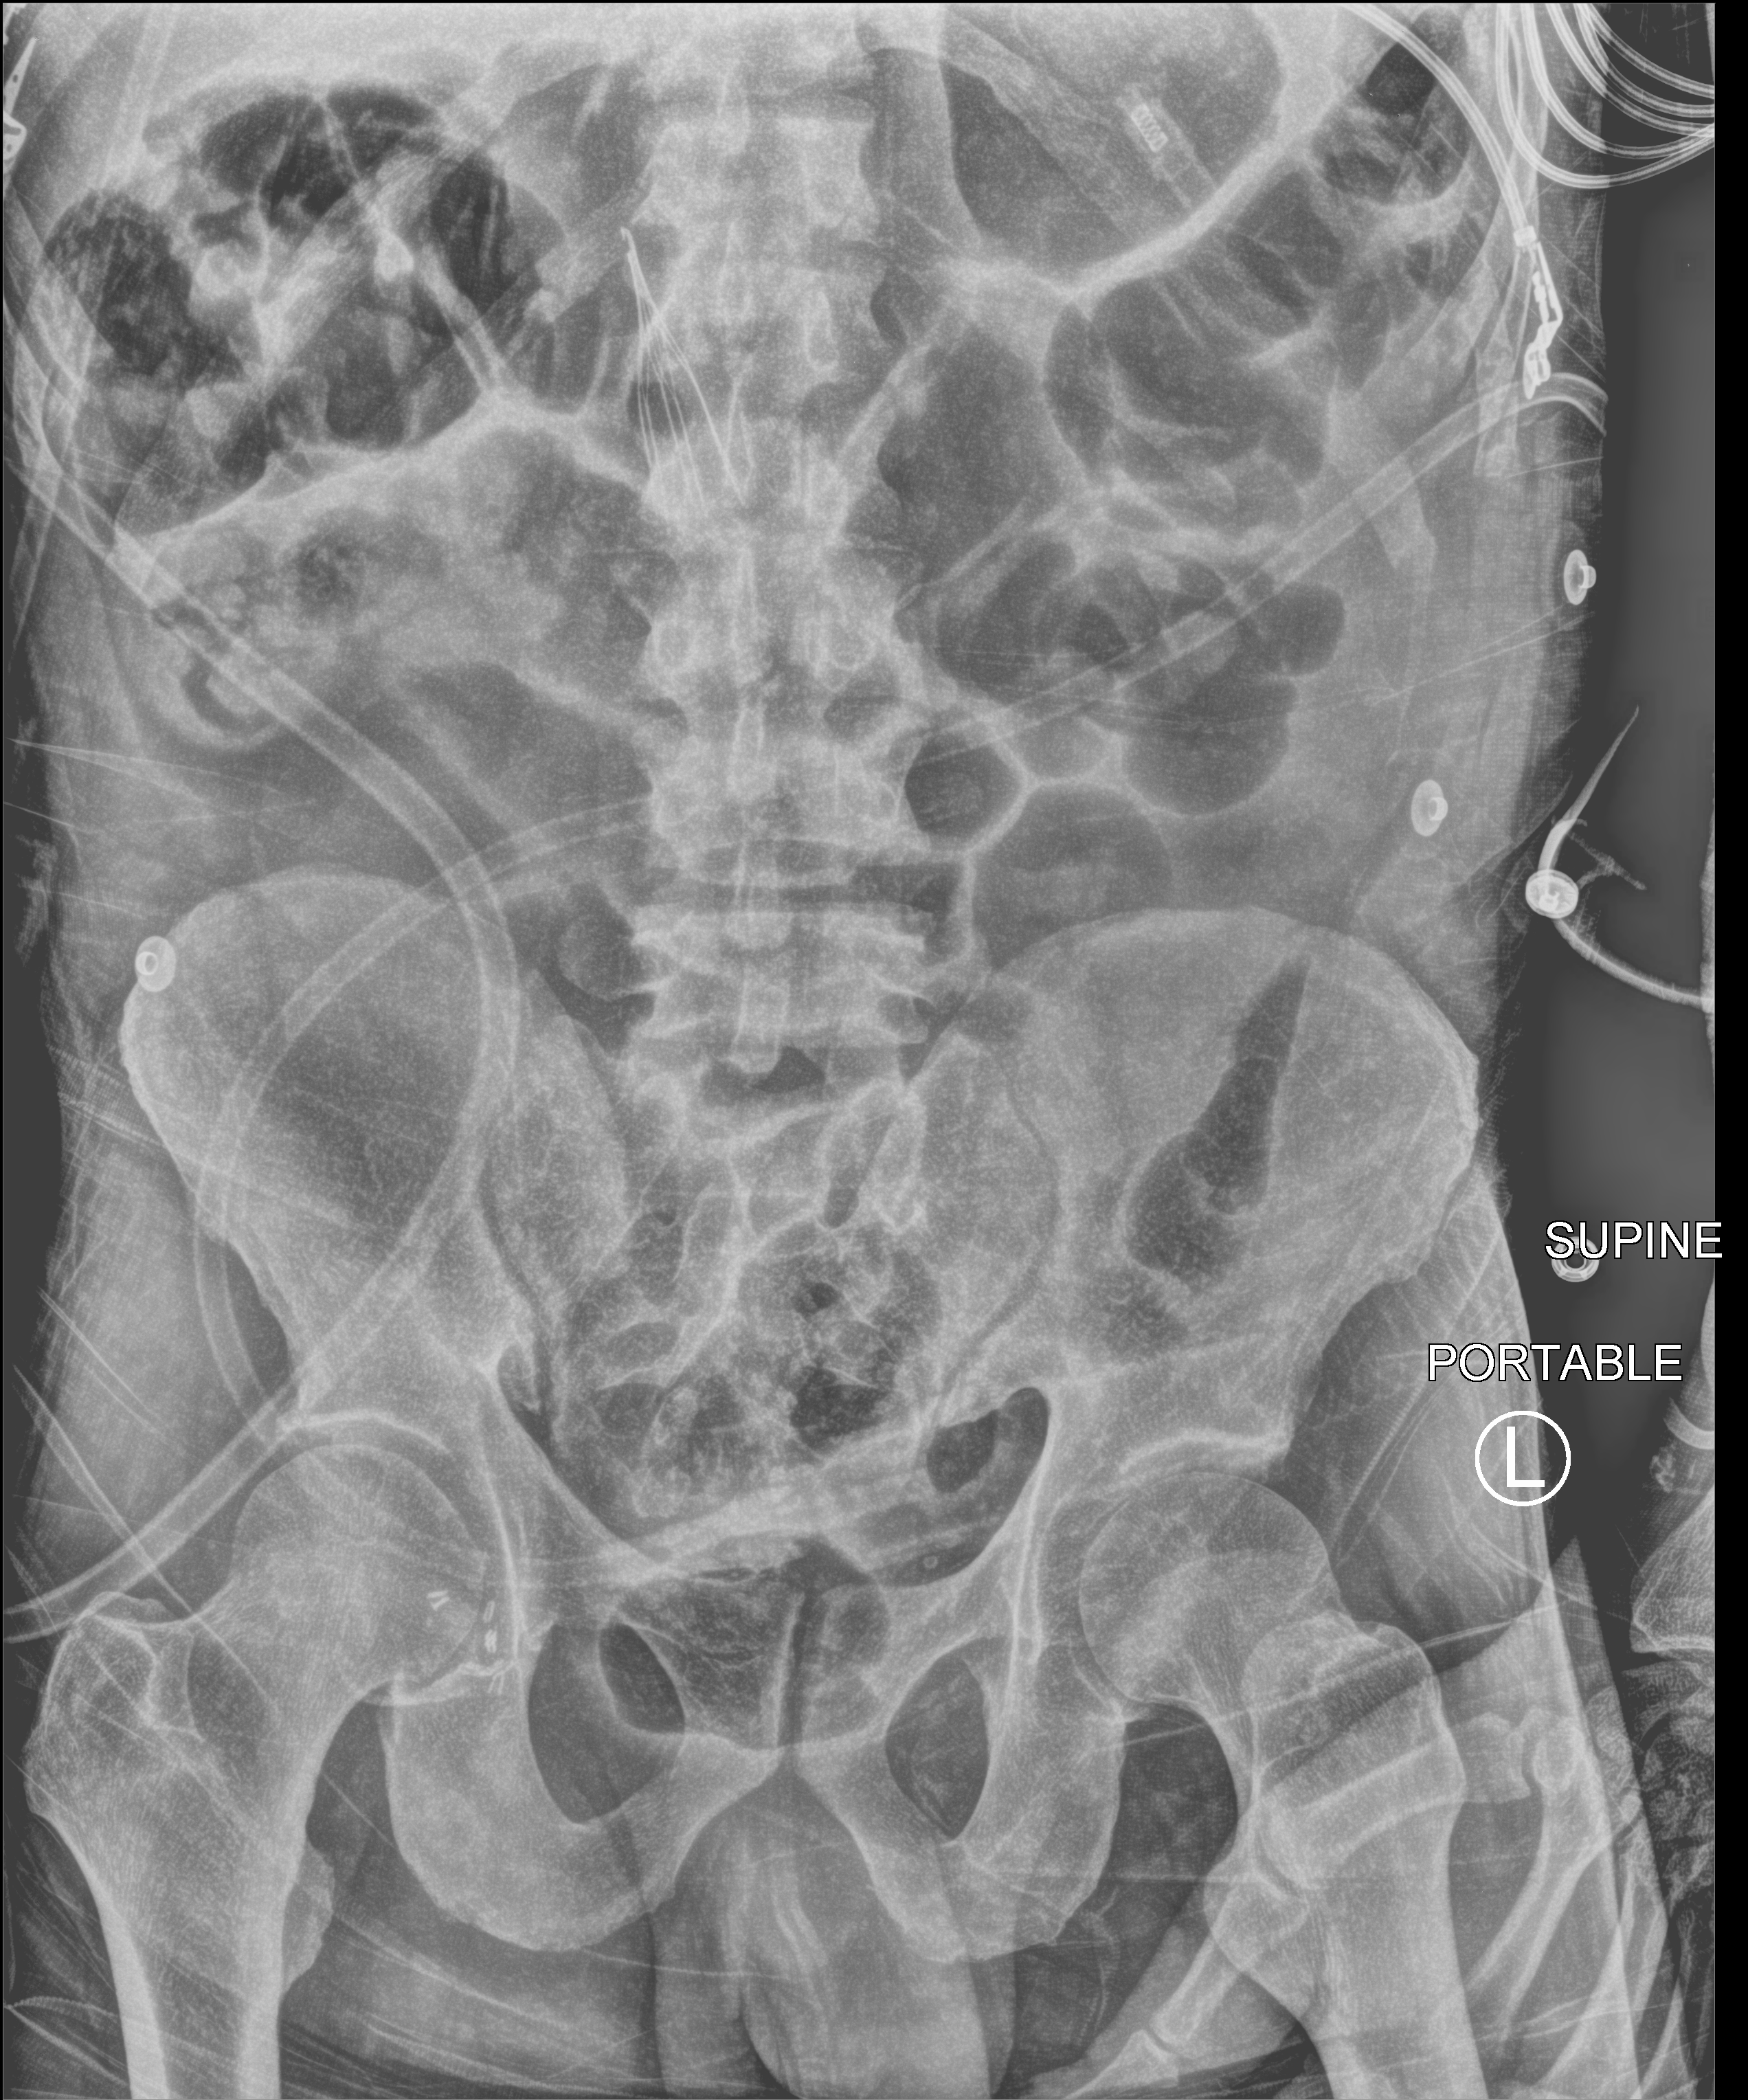
Portable abdomen radiograph, anteroposterior (AP) projection. Male patient hospitalised with COVID-19, age 60–74 years.
Hospital-stay facts (about this admission, not read from this image; timing relative to this image not recorded): length of hospital stay: 50 days; other chronic lung disease (admission record): no.